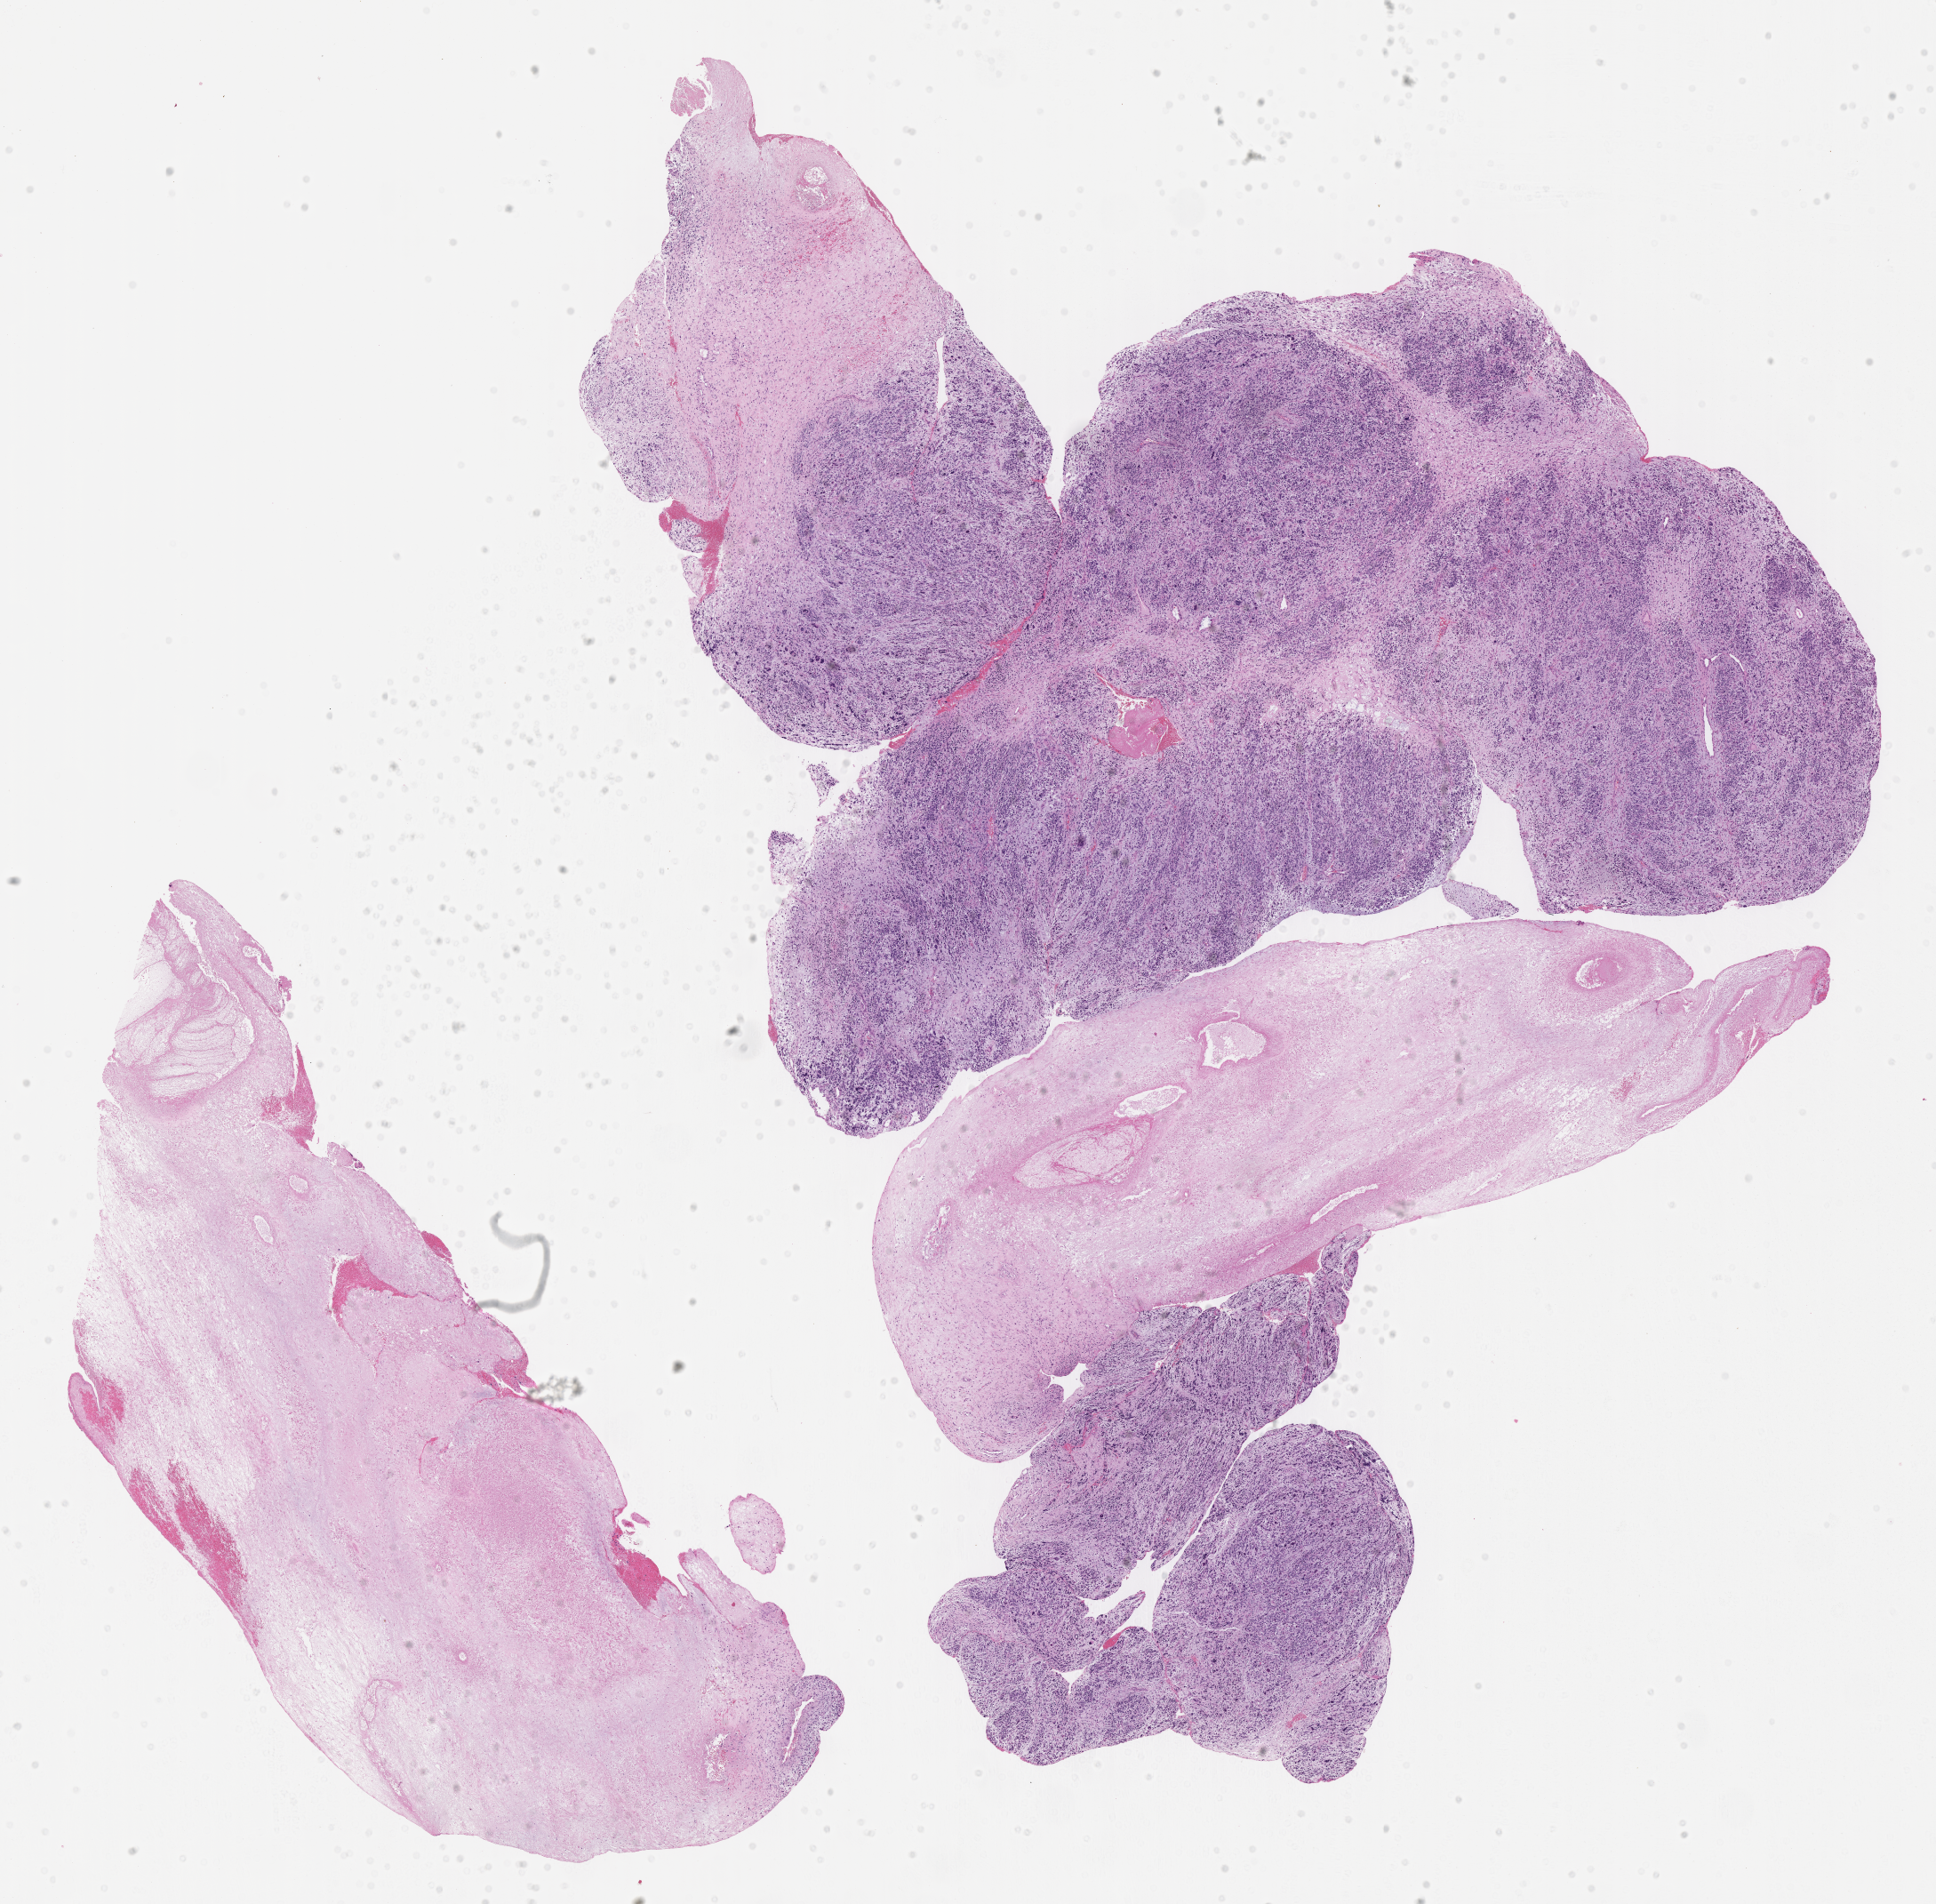
Whole-slide image, hematoxylin and eosin (H&E) stain of tumor tissue — whole scanned area (about 17.6 x 17.3 mm) shown as a low-resolution overview; formalin-fixed paraffin-embedded section; sample anatomic site: soft tissue, thigh-right. Male patient, age at diagnosis 4.4 years.
* metastatic status at presentation (as recorded): non-metastatic (unconfirmed)
* stage (as recorded): 3
* diagnosis: rhabdomyosarcoma; histological classification: embryonal rhabdomyosarcoma